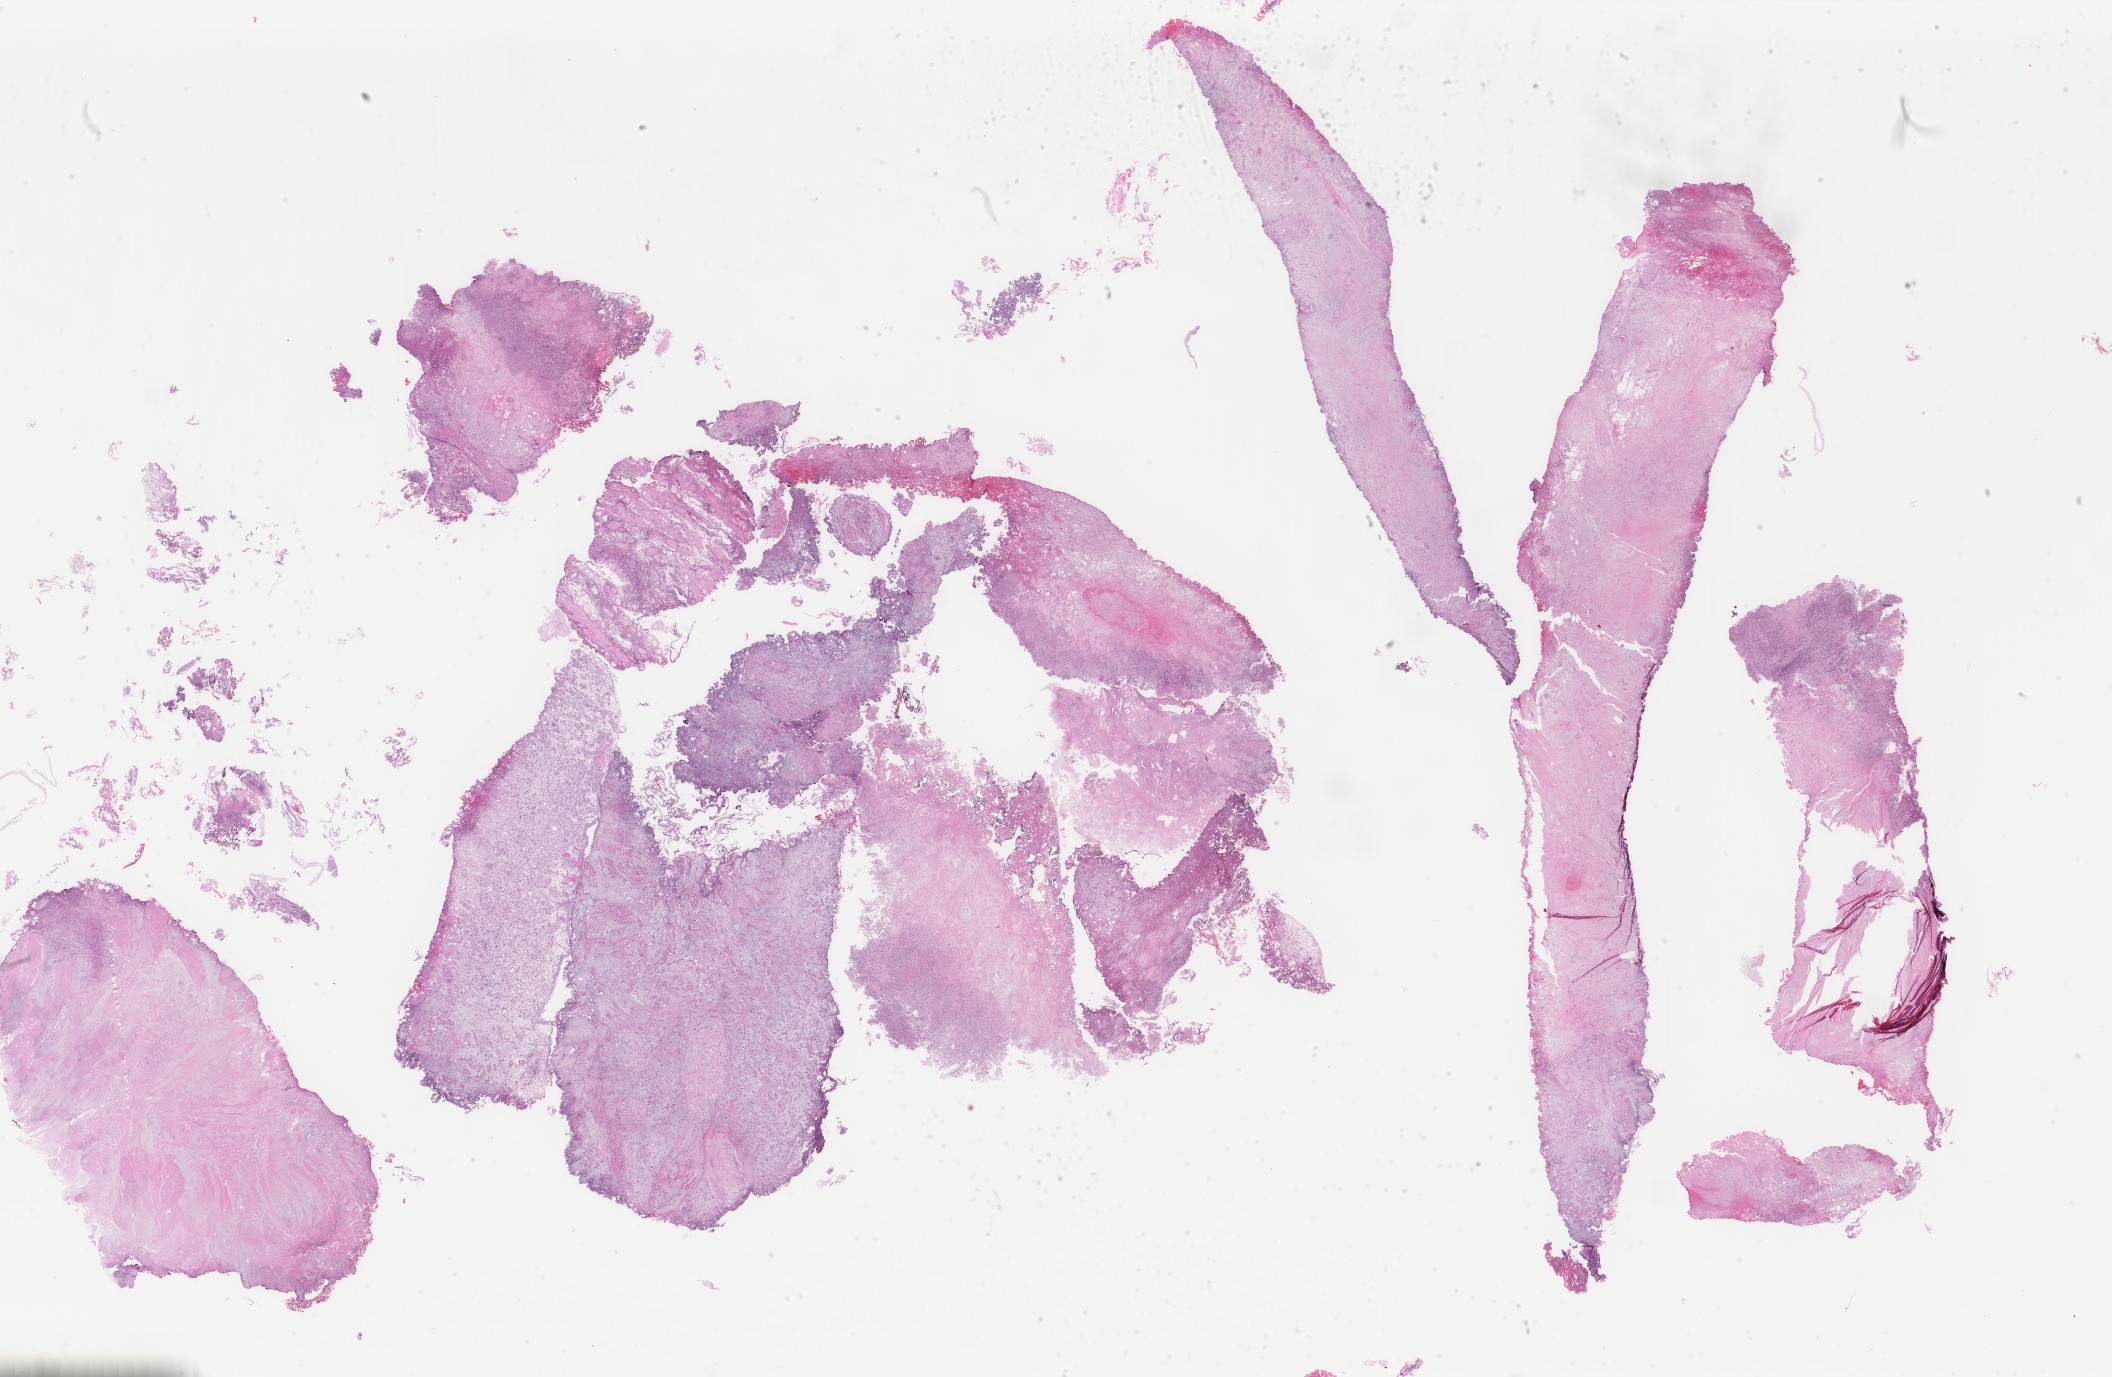
H&E-stained whole-slide image — whole scanned area (about 33.5 x 21.9 mm) shown as a low-resolution overview; formalin-fixed paraffin-embedded (FFPE) diagnostic section; sample: primary tumour, bladder. Female patient; age at initial diagnosis 58 years.
Pathologic diagnosis: Transitional cell carcinoma.